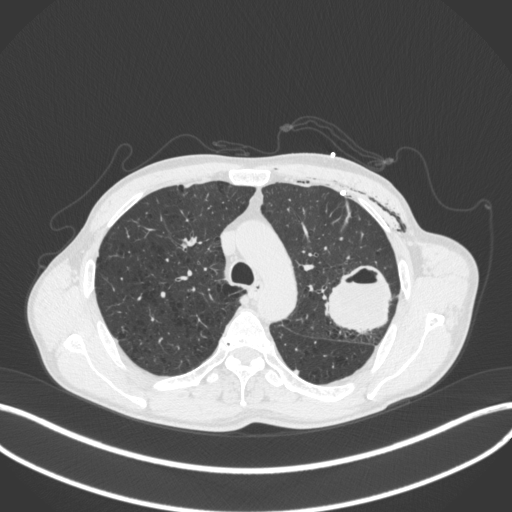
Chest CT, one axial slice. Slice 287 of 416 in the series (ordered by position). Reconstruction kernel B31f. 120 kVp. Lung window (W 1500 / L -600 HU). 1 mm slice thickness. 512 × 512 image matrix. Male patient, age 58 years. Case-level facts recorded for this patient, not image findings: clinical TNM (as recorded): T3 N0 M0.
Outlined on this slice (bounding box drawn by a radiologist):
- lung tumour (recorded histology: adenocarcinoma): box from (x=323, y=262) to (x=399, y=338) px